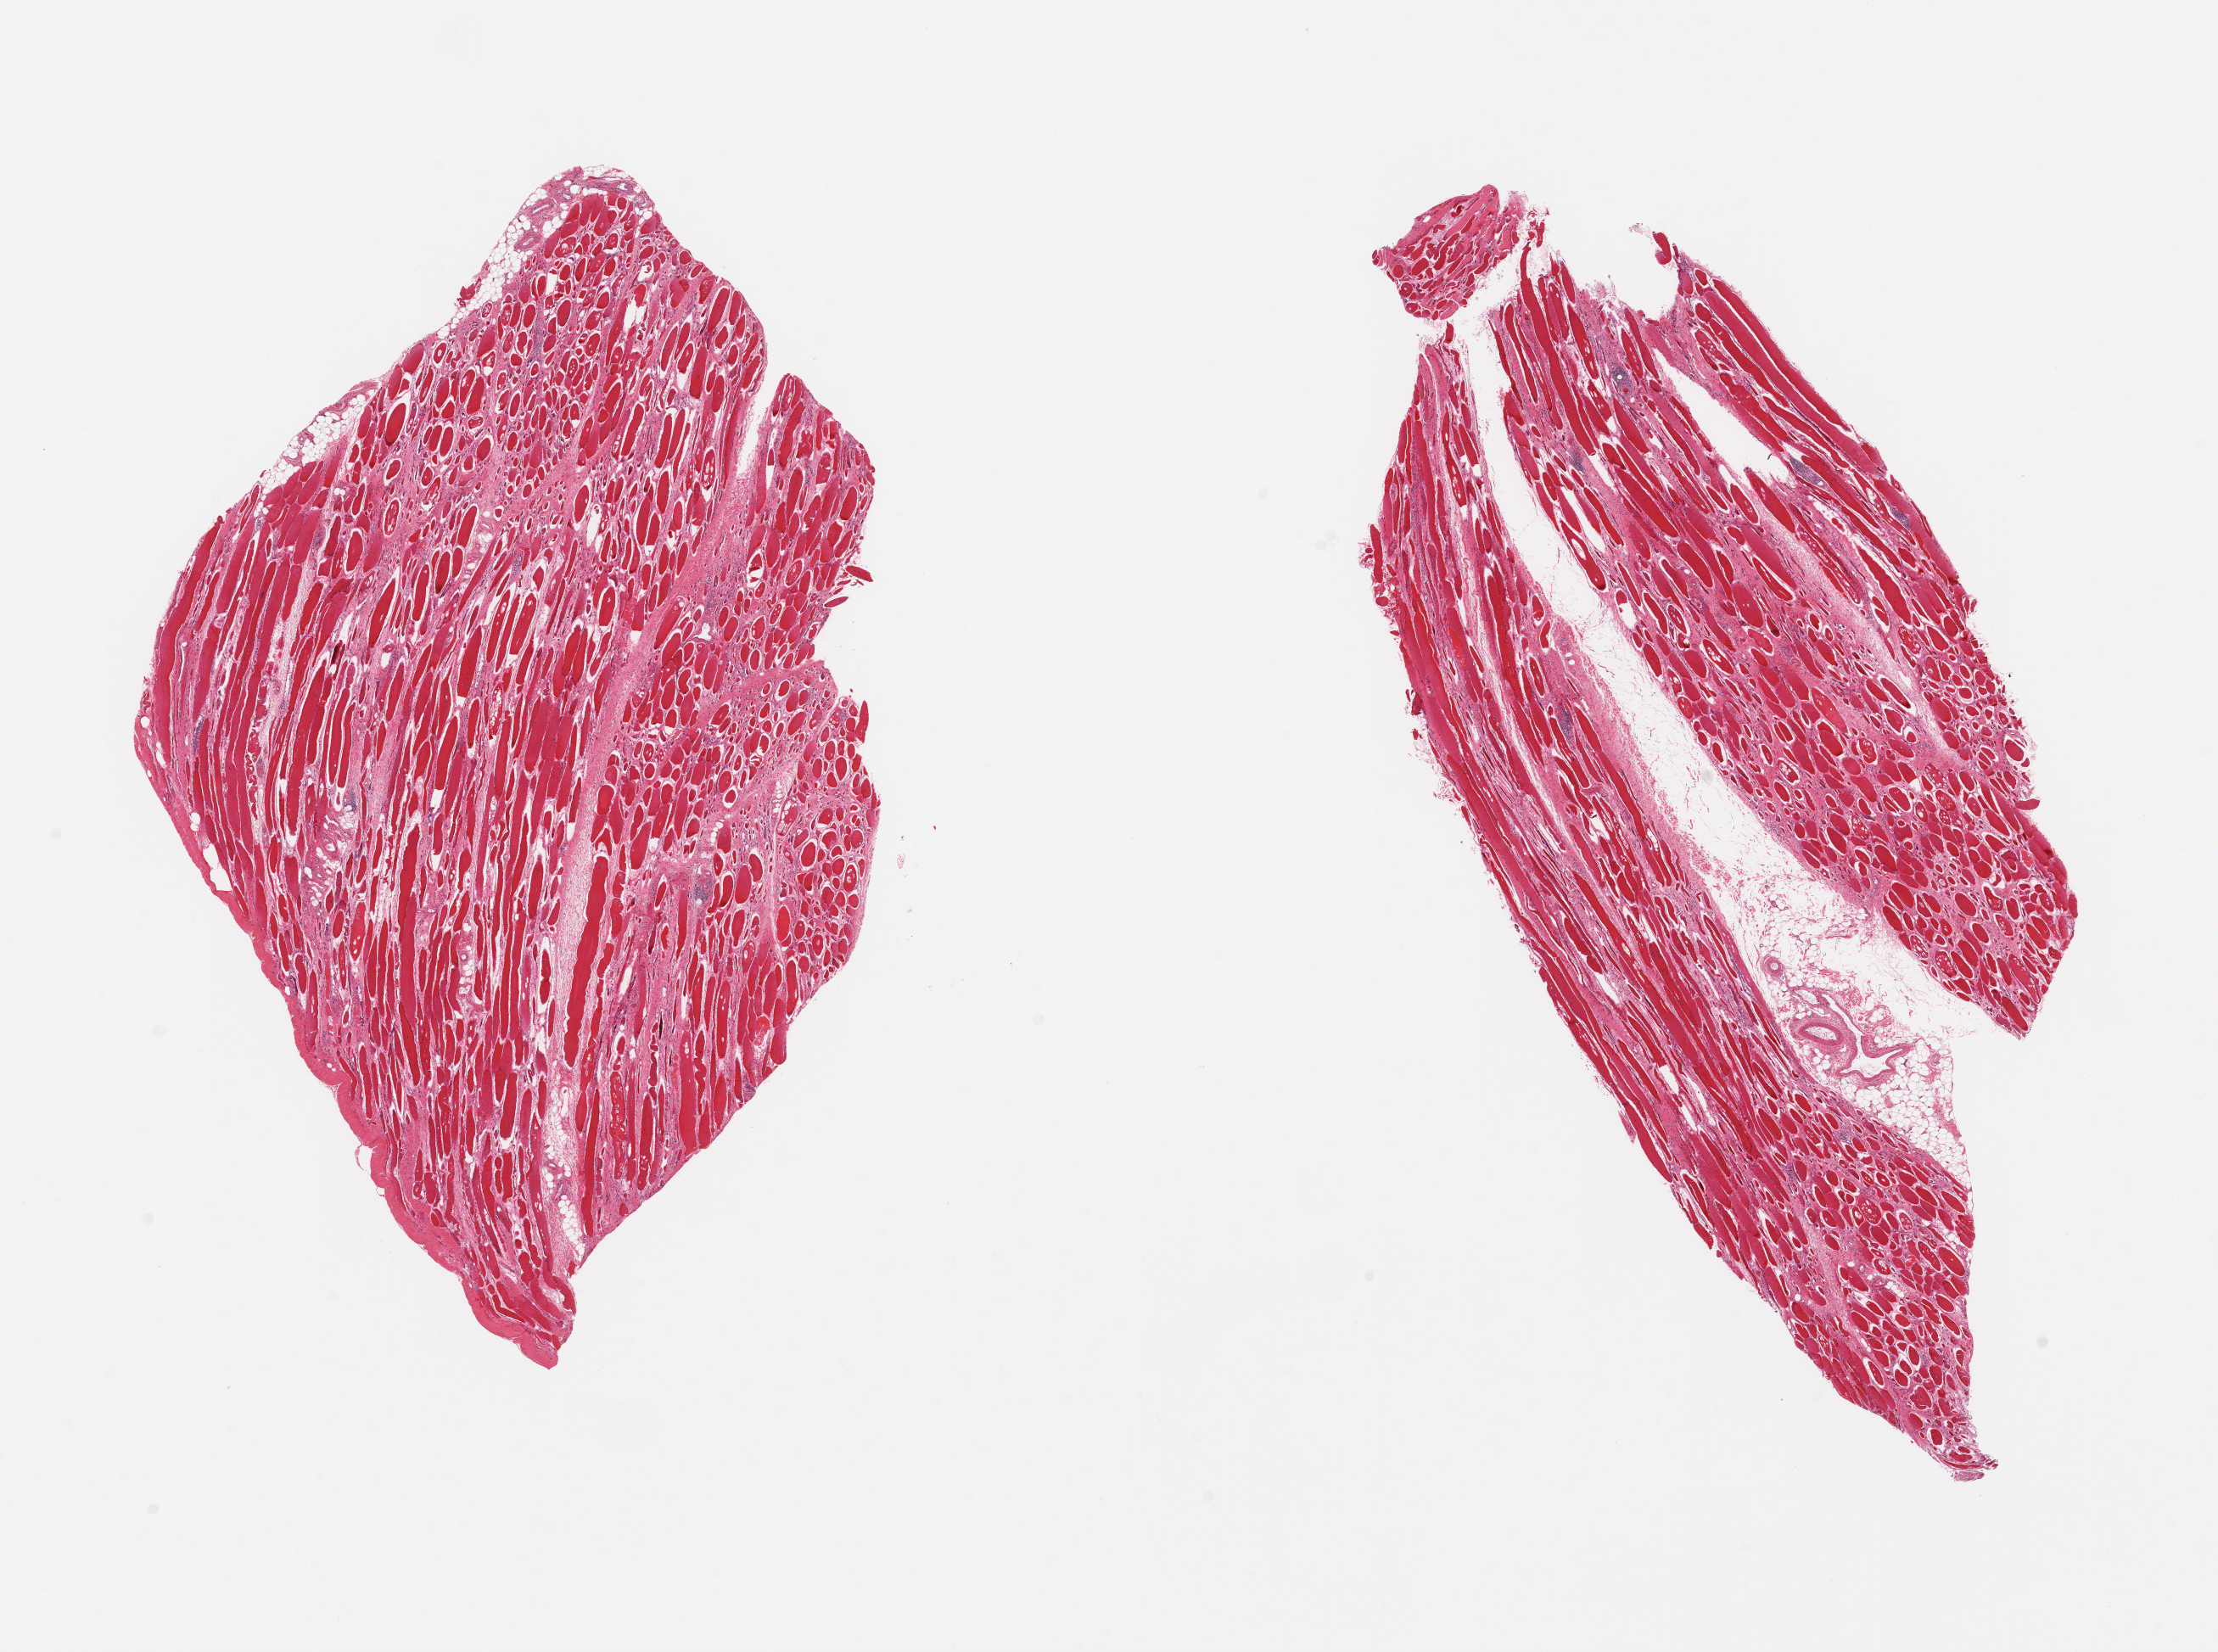
Digitized hematoxylin and eosin (H&E)-stained section, shown as a low-resolution overview of the whole scanned area (about 20.7 x 15.4 mm), PAXgene-fixed paraffin-embedded (PFPE) section, sampled site (target tissue): skeletal muscle, donor tissue sample. Donor sex: female.
Reviewer comment on this tissue sample: 2 pieces; moderate atrophy & fibrosis.